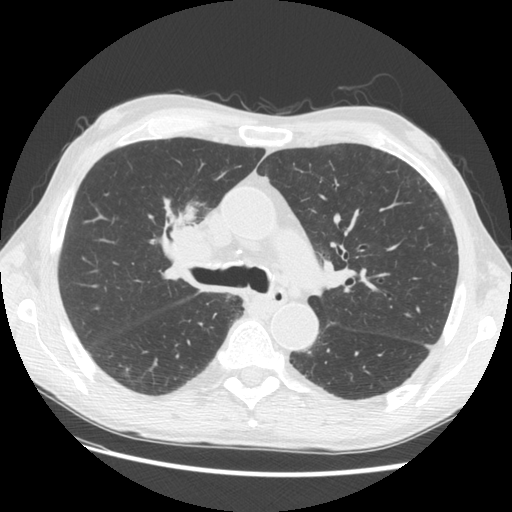
Low-dose screening chest CT, one axial slice; slice 87 of 133 in the series (ordered by position); 120 kVp; lung window (W 1500 / L -600 HU); 2.5 mm slice thickness; 512 × 512 image matrix, field of view 360 × 360 mm.
Structures marked on this image (outlined manually by an expert reader):
- lesion 1 (tumor, hilum of right lung): box from (x=170, y=199) to (x=215, y=239) px